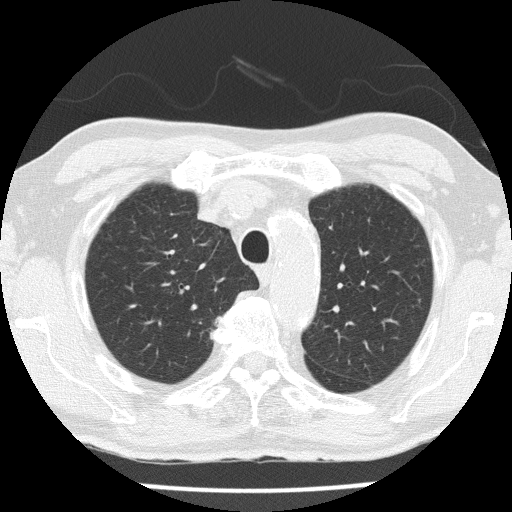
Low-dose screening chest CT, one axial slice. Position 115 of 153 along the scan axis. Reconstruction kernel FC51. Lung window (W 1500 / L -600 HU). 2 mm slice thickness. 512 × 512 image matrix.
Structures marked on this image (manually delineated by an expert):
- lesion 1 (tumor, upper lobe of right lung): bounding box [x1, y1, x2, y2] px = [210, 317, 222, 337]